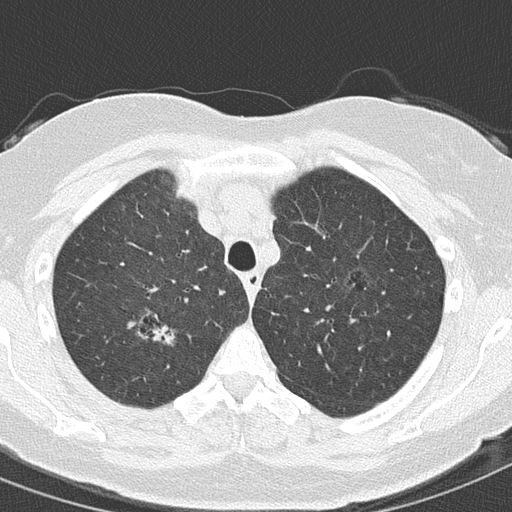
Axial slice from a low-dose chest CT screening exam, second annual screen, lung window (W 1500 / L -600 HU), lung (sharp) reconstruction kernel (B50f), 120 kVp. Female participant, aged 61 years at enrolment.
- Lesion marked by an expert reader, bounding box (x1, y1, x2, y2) in pixels: (145, 312, 187, 351).
- Screening reader's record for this exam (one nodule recorded; not confirmed to be the boxed lesion): non-calcified nodule or mass ≥4 mm, right upper lobe, 15 × 10 mm, spiculated (stellate) margins, ground glass attenuation, pre-existing on the prior screen: yes; interval growth: yes.
- Later outcome: lung cancer diagnosed 91 days after this screen — adenocarcinoma, NOS, right upper lobe, moderately differentiated (G2), stage IA (AJCC 6th edition), 20 mm at pathology.